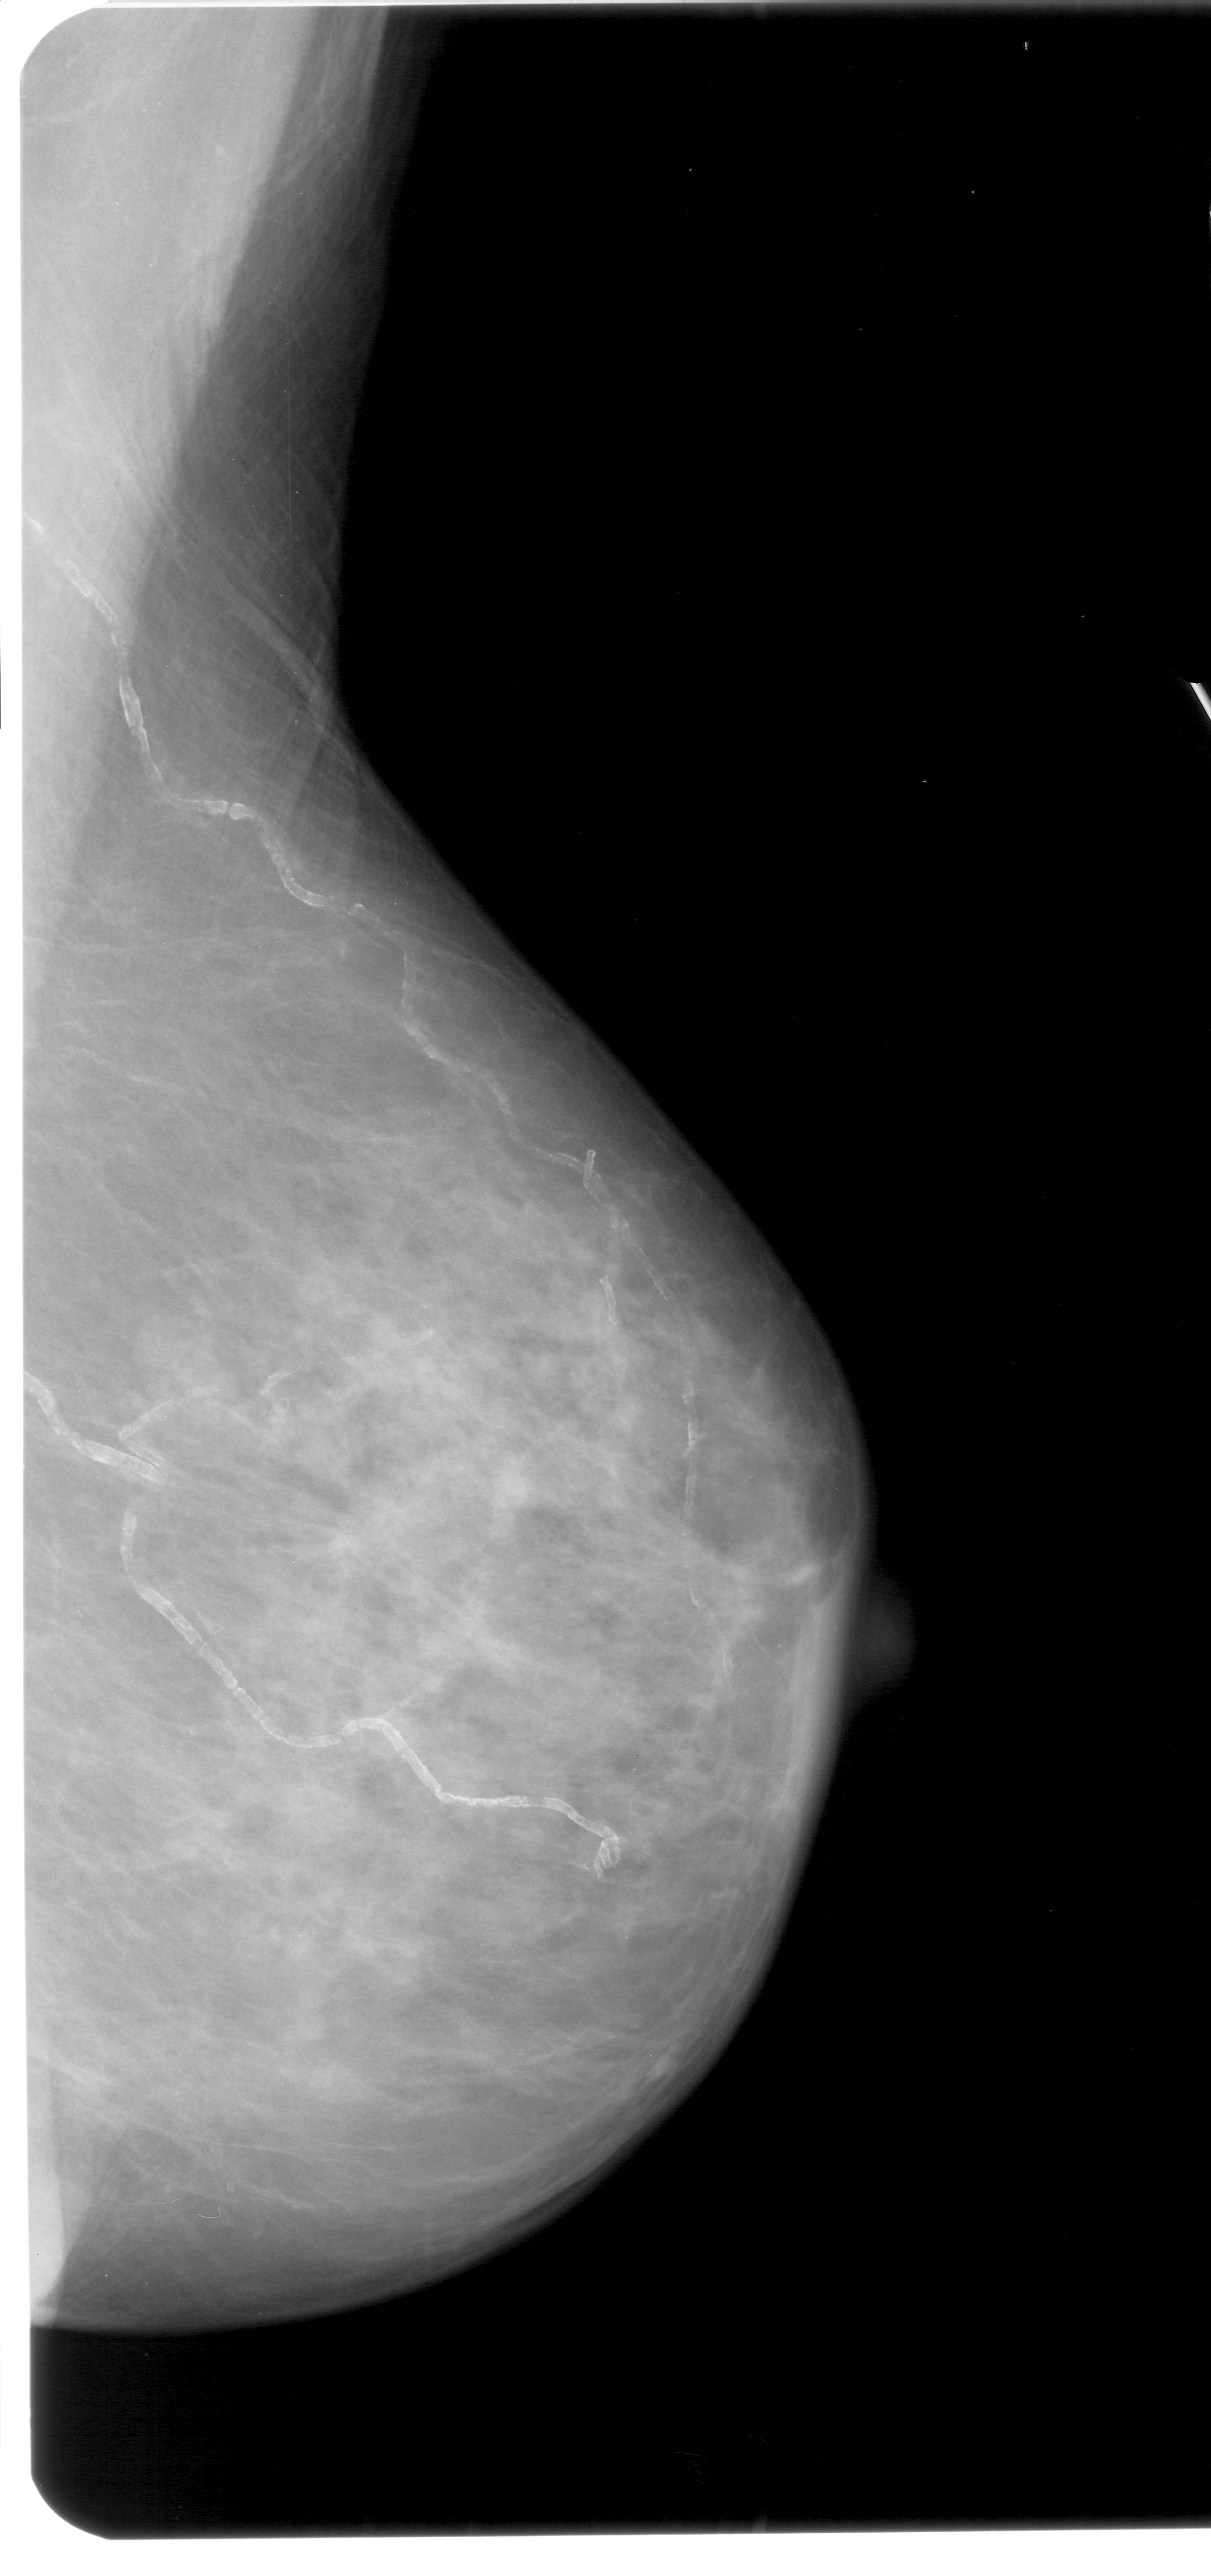
Digitized screen-film mammogram; right breast; mediolateral oblique (MLO) view; breast composition: heterogeneously dense (BI-RADS density category 3 of 4); 1211 × 2576 image matrix.
Expert-marked regions of interest on this image (one box per marked abnormality):
- mass, shape architectural distortion, margins spiculated; BI-RADS assessment category 5; pathology result (as recorded, not read from the image): malignant: bounding box <282,1411,446,1581> (left, top, right, bottom; pixels)